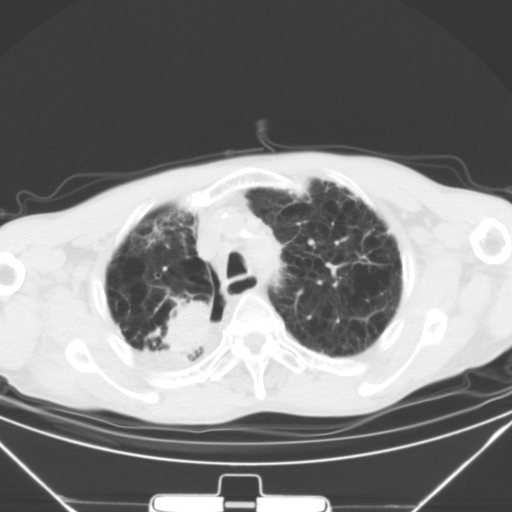
Chest CT, one axial slice. Slice 39 of 50 in the series (ordered by position). Lung window (W 1500 / L -600 HU). 5 mm slice thickness. 512 × 512 image matrix, field of view 373 × 373 mm. Male patient, age 65 years. Case-level facts recorded for this patient, not image findings: clinical TNM (as recorded): T3 N1 M1a.
Outlined on this slice (bounding box drawn by a radiologist):
- lung tumour (recorded histology: squamous cell carcinoma): bounding box (x1, y1, x2, y2) in pixels: (150, 298, 216, 356)